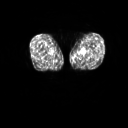
FDG PET of an extremity soft-tissue mass (from a PET/CT study), one axial slice. Slice 5 of 267 in the series (ordered by position). 3.27 mm slice thickness. 128 × 128 image matrix, field of view 600 × 600 mm. Patient: male, 59 years. From the clinical record (not read from this slice): histological type: pleiomorphic liposarcoma; grade: high; site of the primary tumour: left thigh.
Structures marked on this image (expert contour drawn on MRI and transferred to this co-registered scan by the dataset authors):
- gross tumour volume including surrounding oedema: bounding box <80,53,87,58> (left, top, right, bottom; pixels)